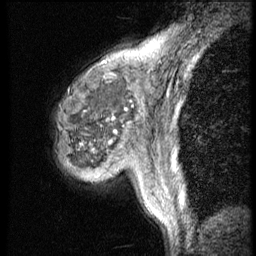
Breast MRI (dynamic contrast-enhanced), one sagittal slice. Position 13 of 56 along the scan axis. 4 images stored at this slice position (order not interpretable as contrast timing). 1.5 T. TE 4.2 ms, TR 9 ms. 2.5 mm slice thickness. 256 × 256 image matrix, field of view 180 × 180 mm. Female patient, age 50 years. From the clinical record (not read from this slice): setting: breast cancer imaged before/during neoadjuvant chemotherapy; receptor status: triple-negative.
Structures marked on this image (semi-automatic segmentation, software-assisted and operator-edited):
- analysis volume of interest (the breast-tissue region the enhancement analysis was run in; not a lesion): bounding box (x1, y1, x2, y2) in pixels: (53, 46, 148, 188)
- tumour enhancement mask (voxels above the 140 % enhancement threshold inside the analysis volume of interest): (114, 50, 138, 134)